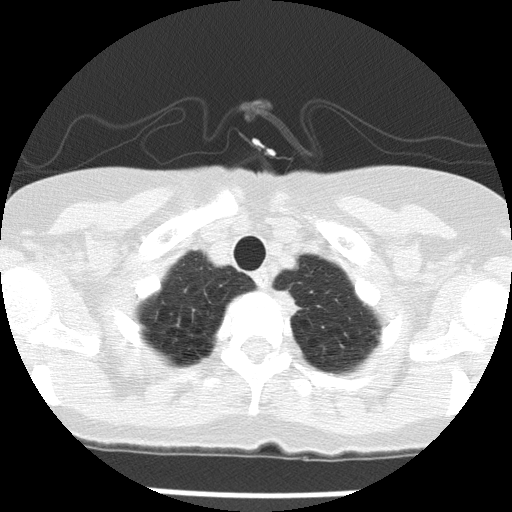
Low-dose screening chest CT, one axial slice; position 130 of 143 along the scan axis; reconstruction kernel FC51; 120 kVp; lung window (W 1500 / L -600 HU); 2 mm slice thickness; 512 × 512 image matrix, field of view 276 × 276 mm.
Outlined on this slice (manually delineated by an expert):
- lesion 1 (tumor, upper lobe of left lung): bounding box [x1, y1, x2, y2] px = [277, 290, 302, 315]